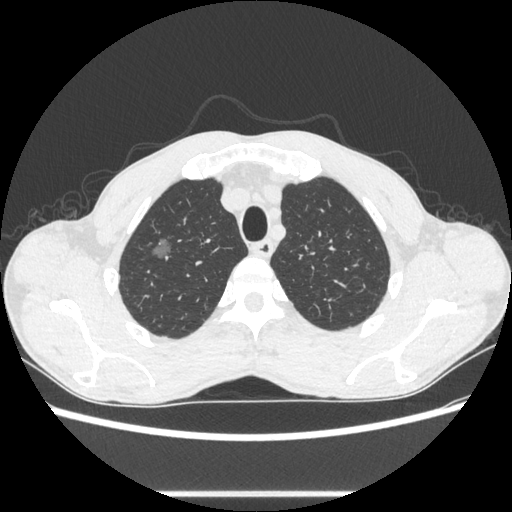
Chest CT, one axial slice; reconstruction kernel STANDARD; lung window (W 1500 / L -600 HU); 0.62 mm slice thickness; 512 × 512 image matrix. Male patient, age 54 years. Case-level facts recorded for this patient, not image findings: clinical TNM (as recorded): T1a N0 M0.
Annotated regions visible in this slice (bounding box drawn by a radiologist):
- lung tumour (recorded histology: adenocarcinoma): bounding box (x1, y1, x2, y2) in pixels: (143, 234, 183, 275)